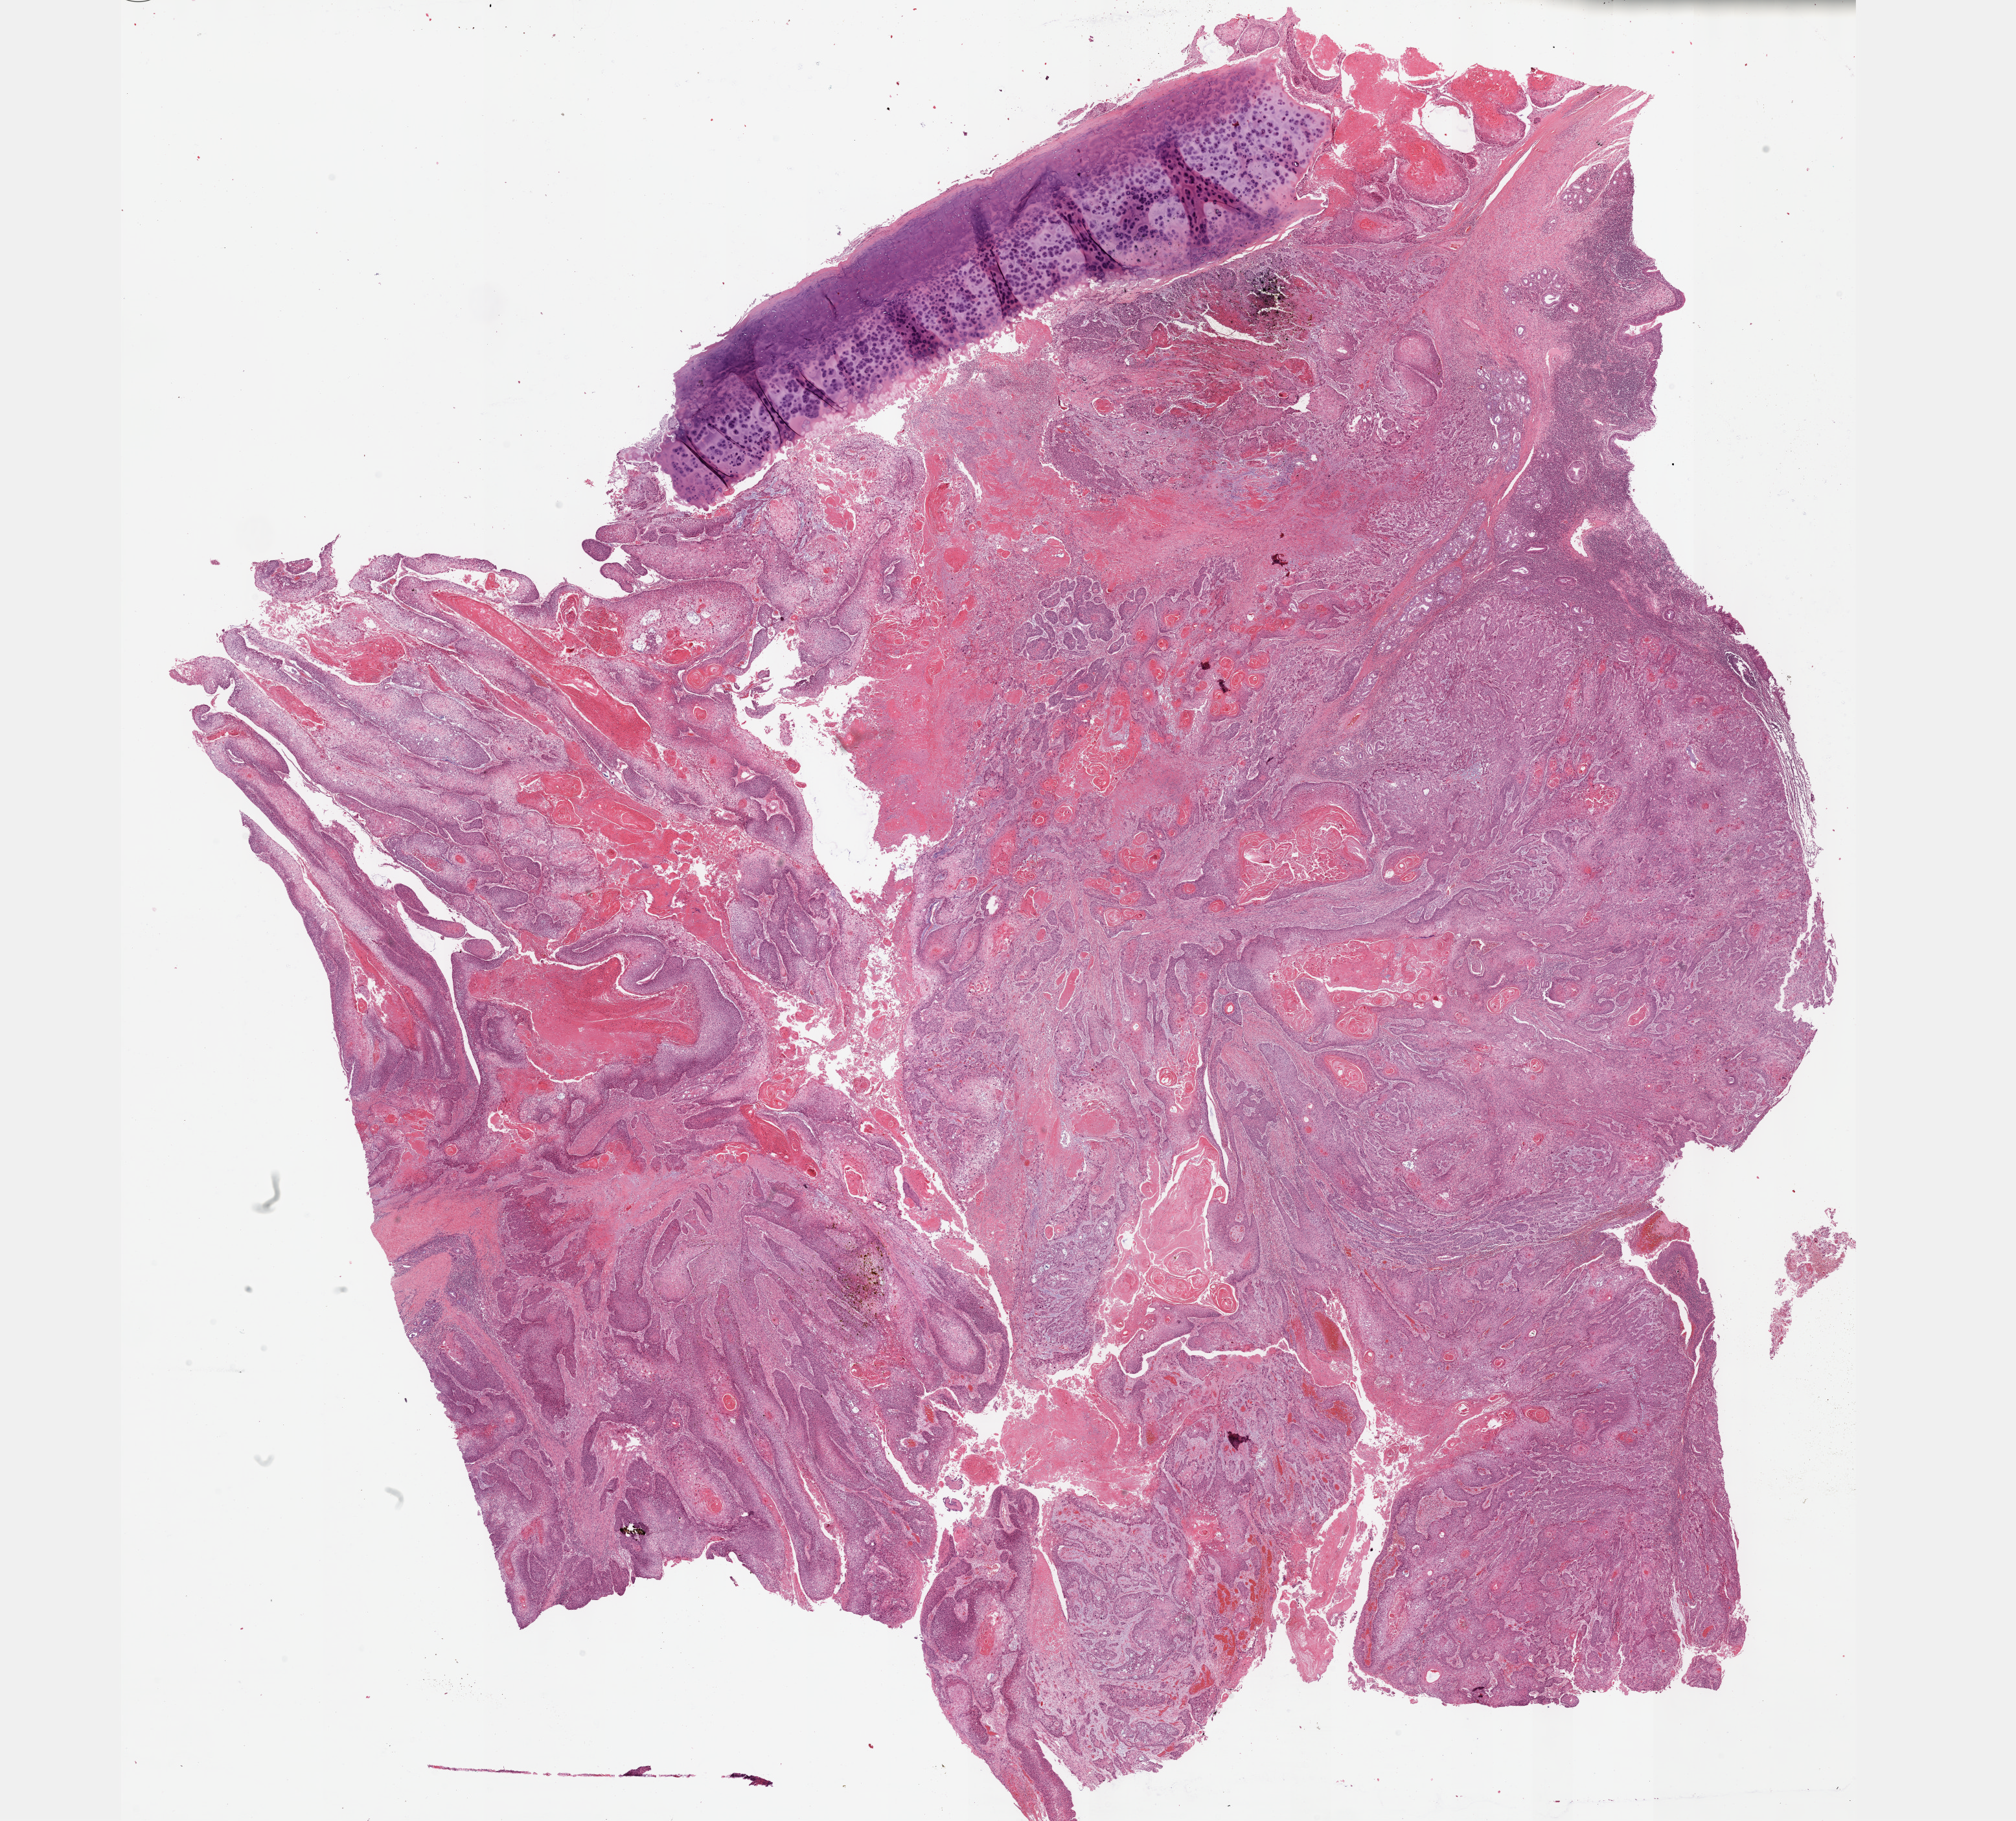
H&E-stained whole-slide image, low-resolution overview of the scanned area, about 25.1 x 22.7 mm, FFPE section, primary tumour sample from the head and neck. Male patient; age at initial diagnosis 59 years.
Pathologic diagnosis: Squamous cell carcinoma, NOS (larynx, NOS).